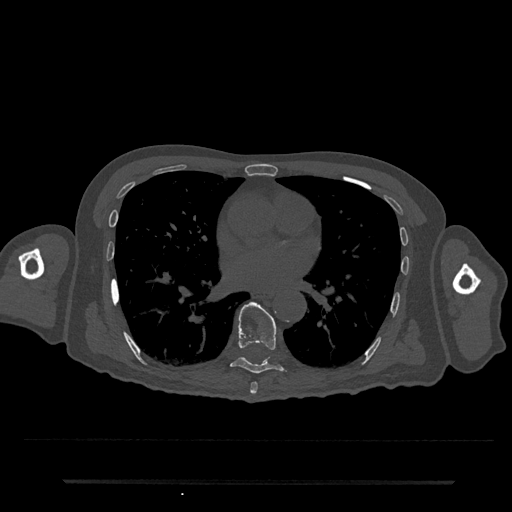
CT including the spine, one axial slice. Slice 424 of 797 in the series (ordered by position). 120 kVp. Bone window (W 1800 / L 400 HU). 512 × 512 image matrix, field of view 427 × 427 mm. Male patient, age 74 years. Case-level facts recorded for this patient, not image findings: primary cancer: prostate.
Outlined on this slice (semi-automatically segmented with operator editing):
- T7 vertebra: bounding box [x1, y1, x2, y2] px = [250, 382, 258, 395]
- T8 vertebra: [230, 302, 286, 374]